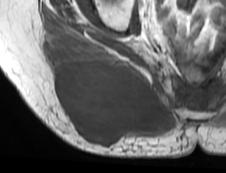
MRI of an extremity soft-tissue mass, one axial slice. Slice 35 of 73 in the series (ordered by position). MR volume resampled by the dataset authors to the PET/CT grid (not the native acquisition matrix). 3.27 mm slice thickness. 226 × 173 image matrix, field of view 221 × 169 mm. Female patient. Case-level facts recorded for this patient, not image findings: histological type: spindle cell suggestive of myxofibrosarcoma; grade: intermediate; site of the primary tumour: right buttock.
Outlined on this slice (expert contour drawn on MRI and transferred to this co-registered scan by the dataset authors):
- gross tumour volume (mass): bounding box <50,49,163,146> (left, top, right, bottom; pixels)